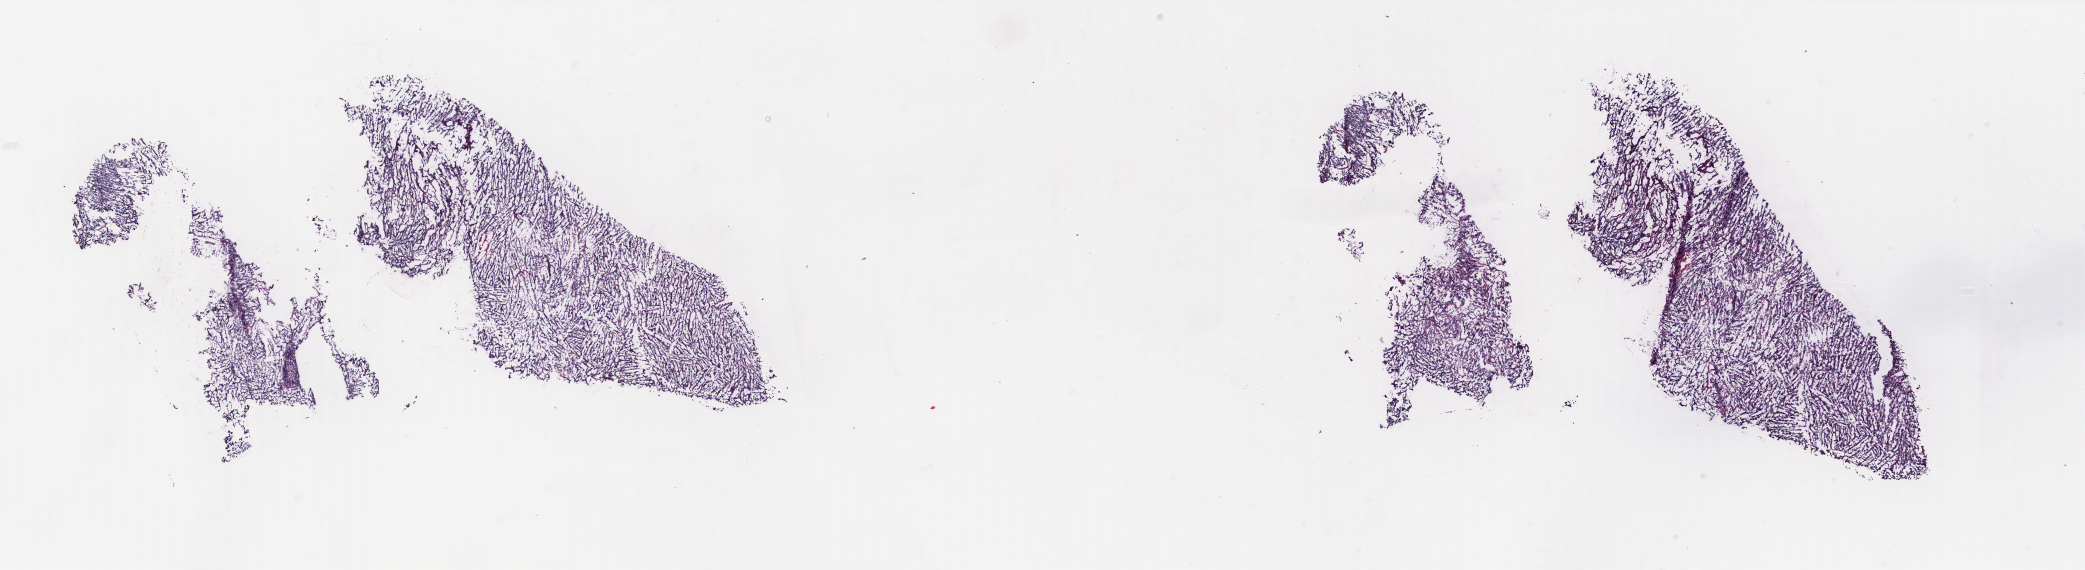
H&E whole-slide image, shown as a low-resolution overview of the whole scanned area (about 33.4 x 9.1 mm, from a 40x scan); frozen section; primary tumour sample from the uterus. Female patient; age at initial diagnosis 71 years. Histologic grade: G3 (poorly differentiated). Composition of this section per pathologist review: tumour cells 80%, tumour nuclei 100%, normal cells 0%, stromal cells 0%, necrosis 20%. Infiltration values recorded for this section: lymphocyte infiltration 20%, monocyte infiltration 0%, neutrophil infiltration 20%.
FIGO stage: IA. Pathologic diagnosis: Serous cystadenocarcinoma, NOS (endometrium).